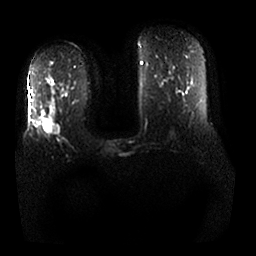
Breast MRI, one axial slice; slice 13 of 25 in the series (ordered by position); diffusion-weighted series; image 2 of 4 stored at this slice position (different b-values; order by instance number); 1.5 T; 4 mm slice thickness; 256 × 256 image matrix, field of view 380 × 380 mm. Female patient.
Annotated regions visible in this slice (manually delineated by an expert):
- tumour on diffusion-weighted imaging: bounding box <43,122,59,137> (left, top, right, bottom; pixels)